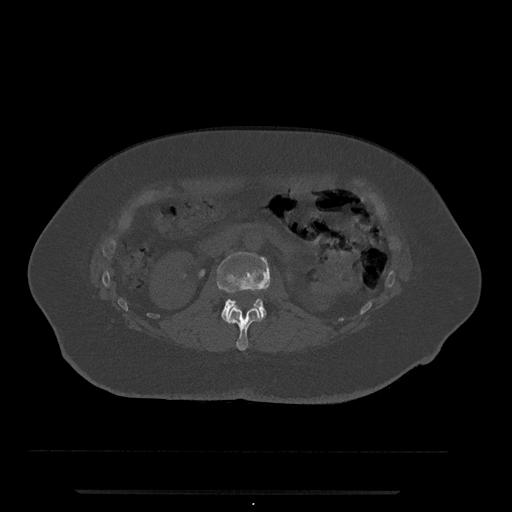
CT including the spine, one axial slice; slice 66 of 797 in the series (ordered by position); reconstruction kernel Br40s/3; 120 kVp; bone window (W 1800 / L 400 HU); 0.5 mm slice thickness; 512 × 512 image matrix. Patient: female, 51 years. From the clinical record (not read from this slice): primary cancer: neuro.
Structures marked on this image (semi-automatically segmented with operator editing):
- L1 vertebra: bounding box <225,307,261,351> (left, top, right, bottom; pixels)
- L2 vertebra: <217,252,270,321>